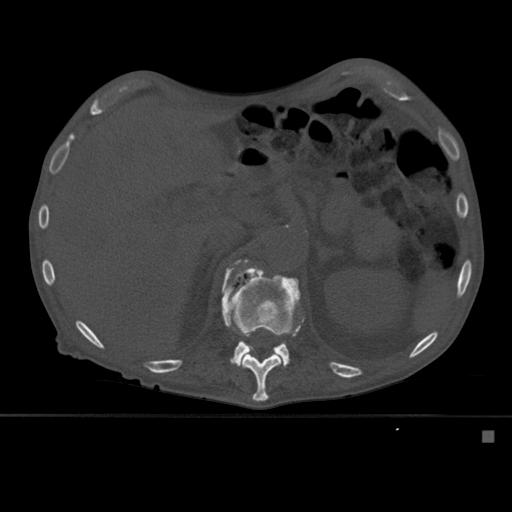
CT including the spine, one axial slice; slice 268 of 527 in the series (ordered by position); bone window (W 1800 / L 400 HU); 1.5 mm slice thickness; 512 × 512 image matrix, field of view 373 × 373 mm. Male patient, age 78 years. Case-level facts recorded for this patient, not image findings: primary cancer: prostate.
Annotated regions visible in this slice (semi-automatic segmentation, software-assisted and operator-edited):
- L1 vertebra: bounding box (x1, y1, x2, y2) in pixels: (222, 266, 300, 367)
- T12 vertebra: (222, 259, 304, 401)